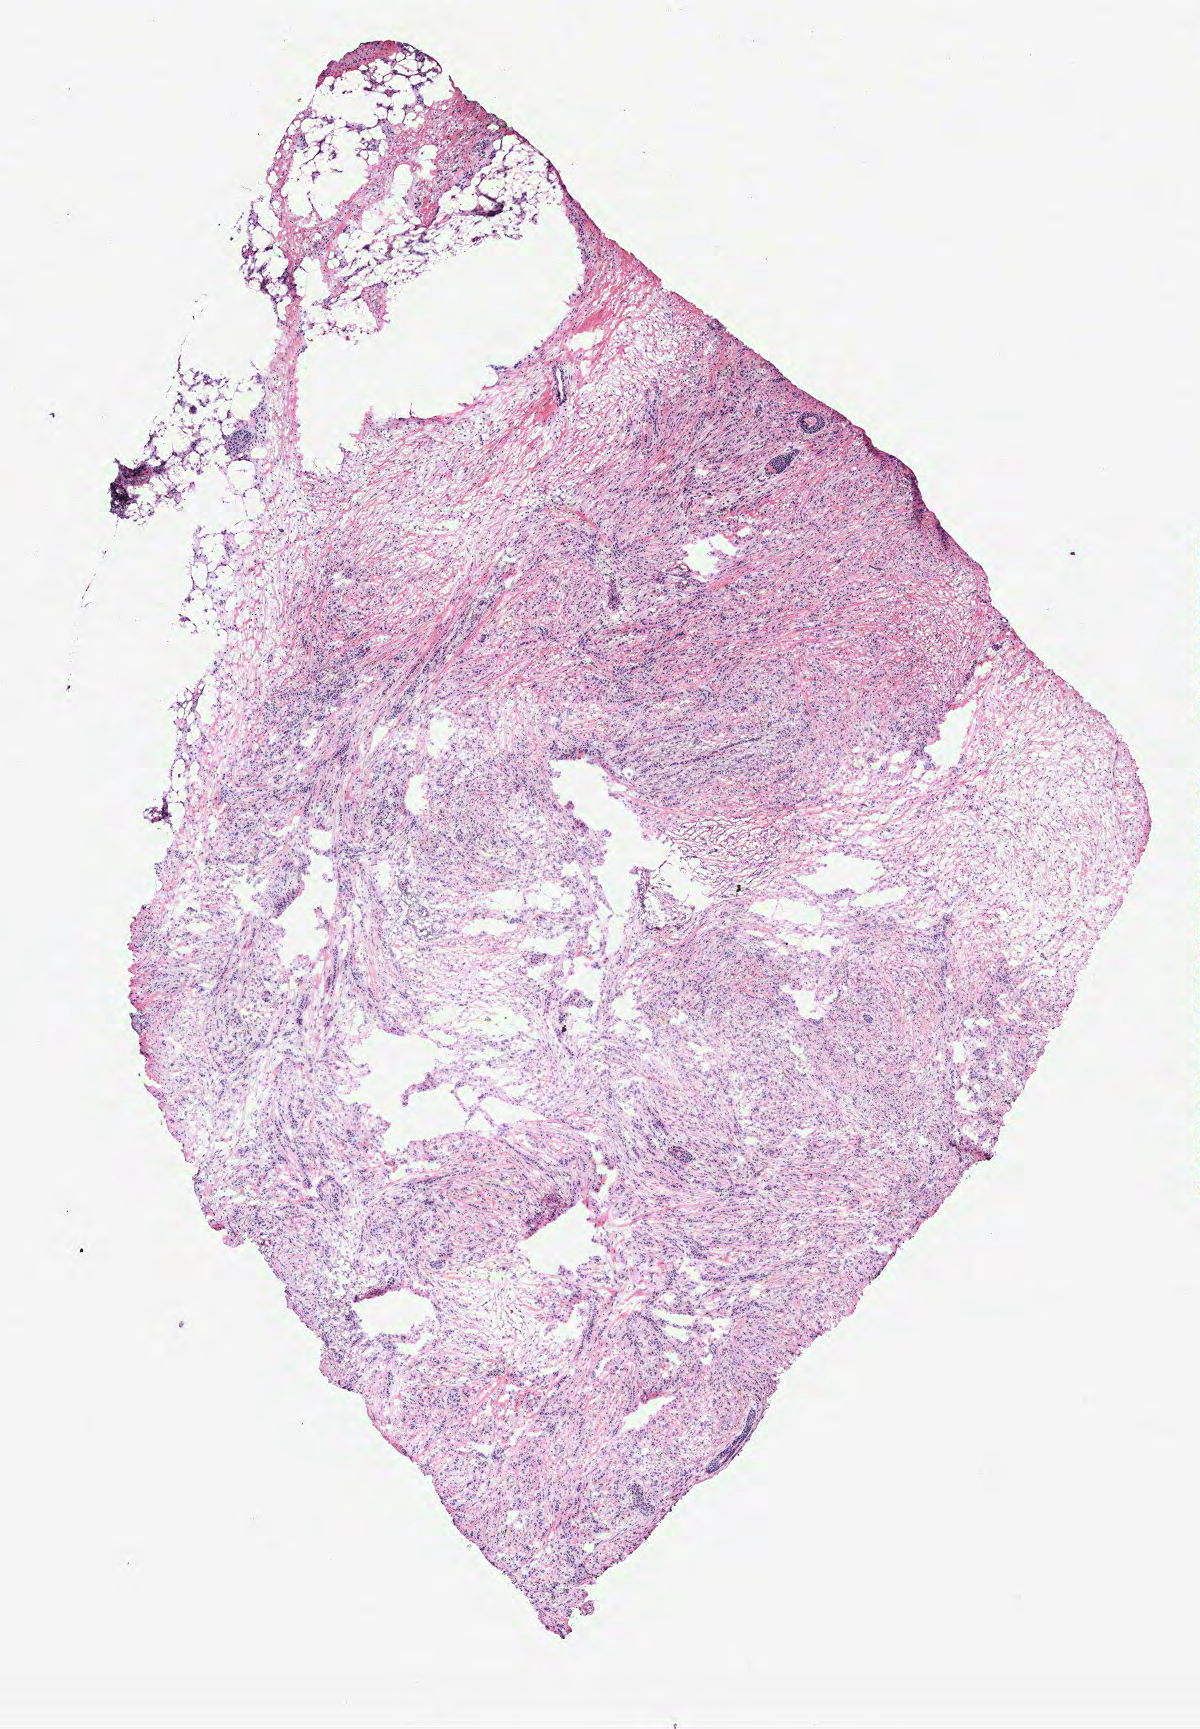
Digitized H&E-stained tissue section (whole slide) — shown as a low-resolution overview of the whole scanned area (about 4.8 x 6.9 mm, slide scanned at 40x), breast, tissue type not recorded. Patient: female, age 46 years.
Patient diagnosis: Infiltrating duct carcinoma, NOS.